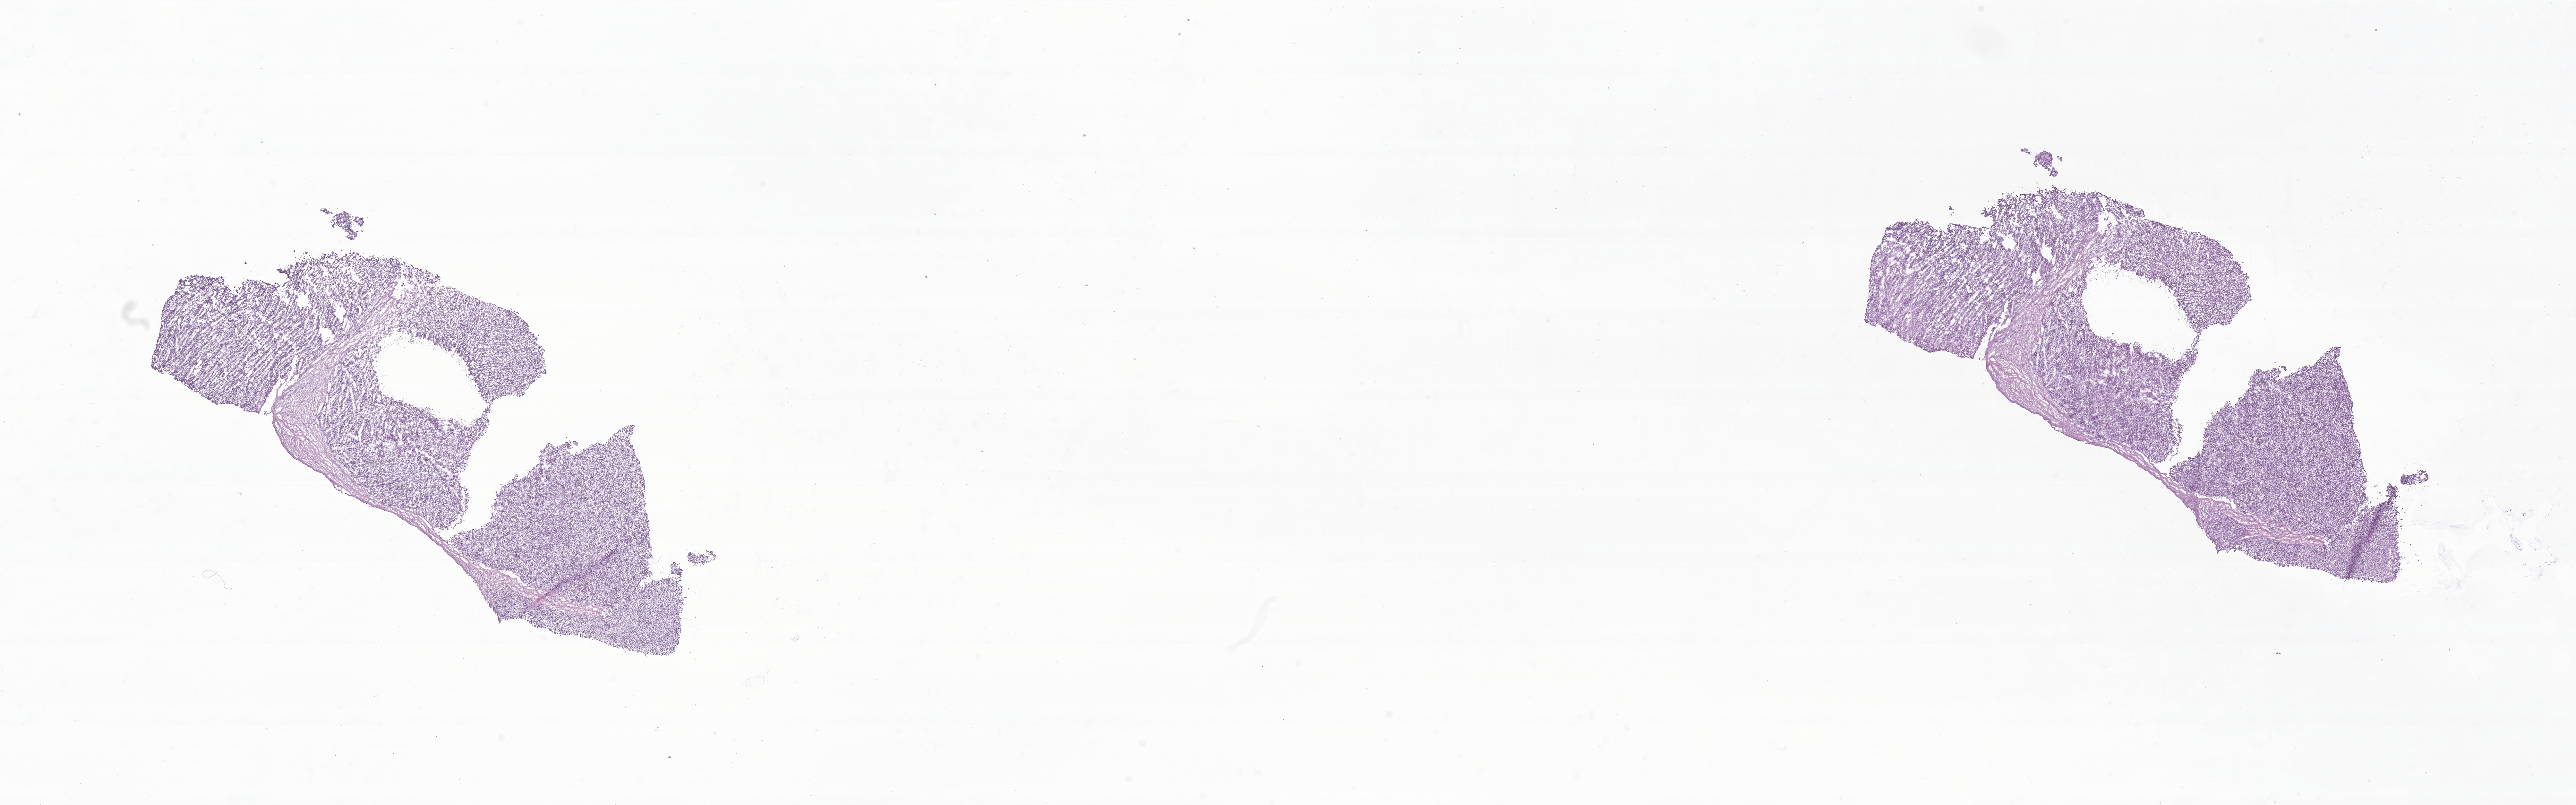
Whole-slide image, hematoxylin and eosin (H&E) stain of tumor tissue from the soft tissue — shown as a low-resolution overview of the whole scanned area (about 33.9 x 10.6 mm); frozen section (OCT-embedded). Patient male; age 189 months (15 years 9 months).
Diagnosis (ICD-O-3 morphology term): Embryonal rhabdomyosarcoma, NOS.